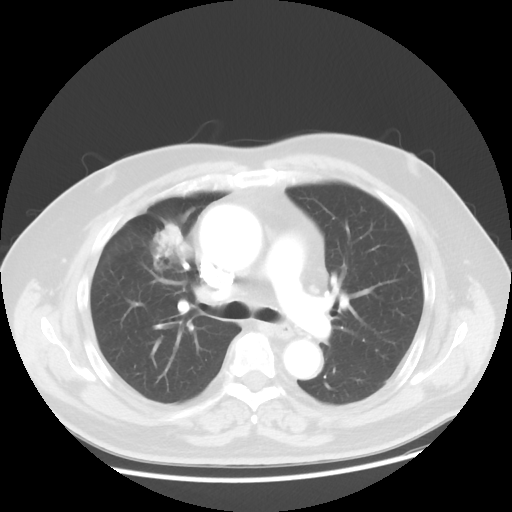
Chest CT, one axial slice; reconstruction kernel STANDARD; 120 kVp; lung window (W 1500 / L -600 HU); 512 × 512 image matrix. Patient: male, 60 years. From the clinical record (not read from this slice): clinical TNM (as recorded): T2 N3 M0; histopathological grade: G2-3.
Annotated regions visible in this slice (bounding box drawn by a radiologist):
- lung tumour (recorded histology: adenocarcinoma): bounding box (x1, y1, x2, y2) in pixels: (143, 219, 195, 285)